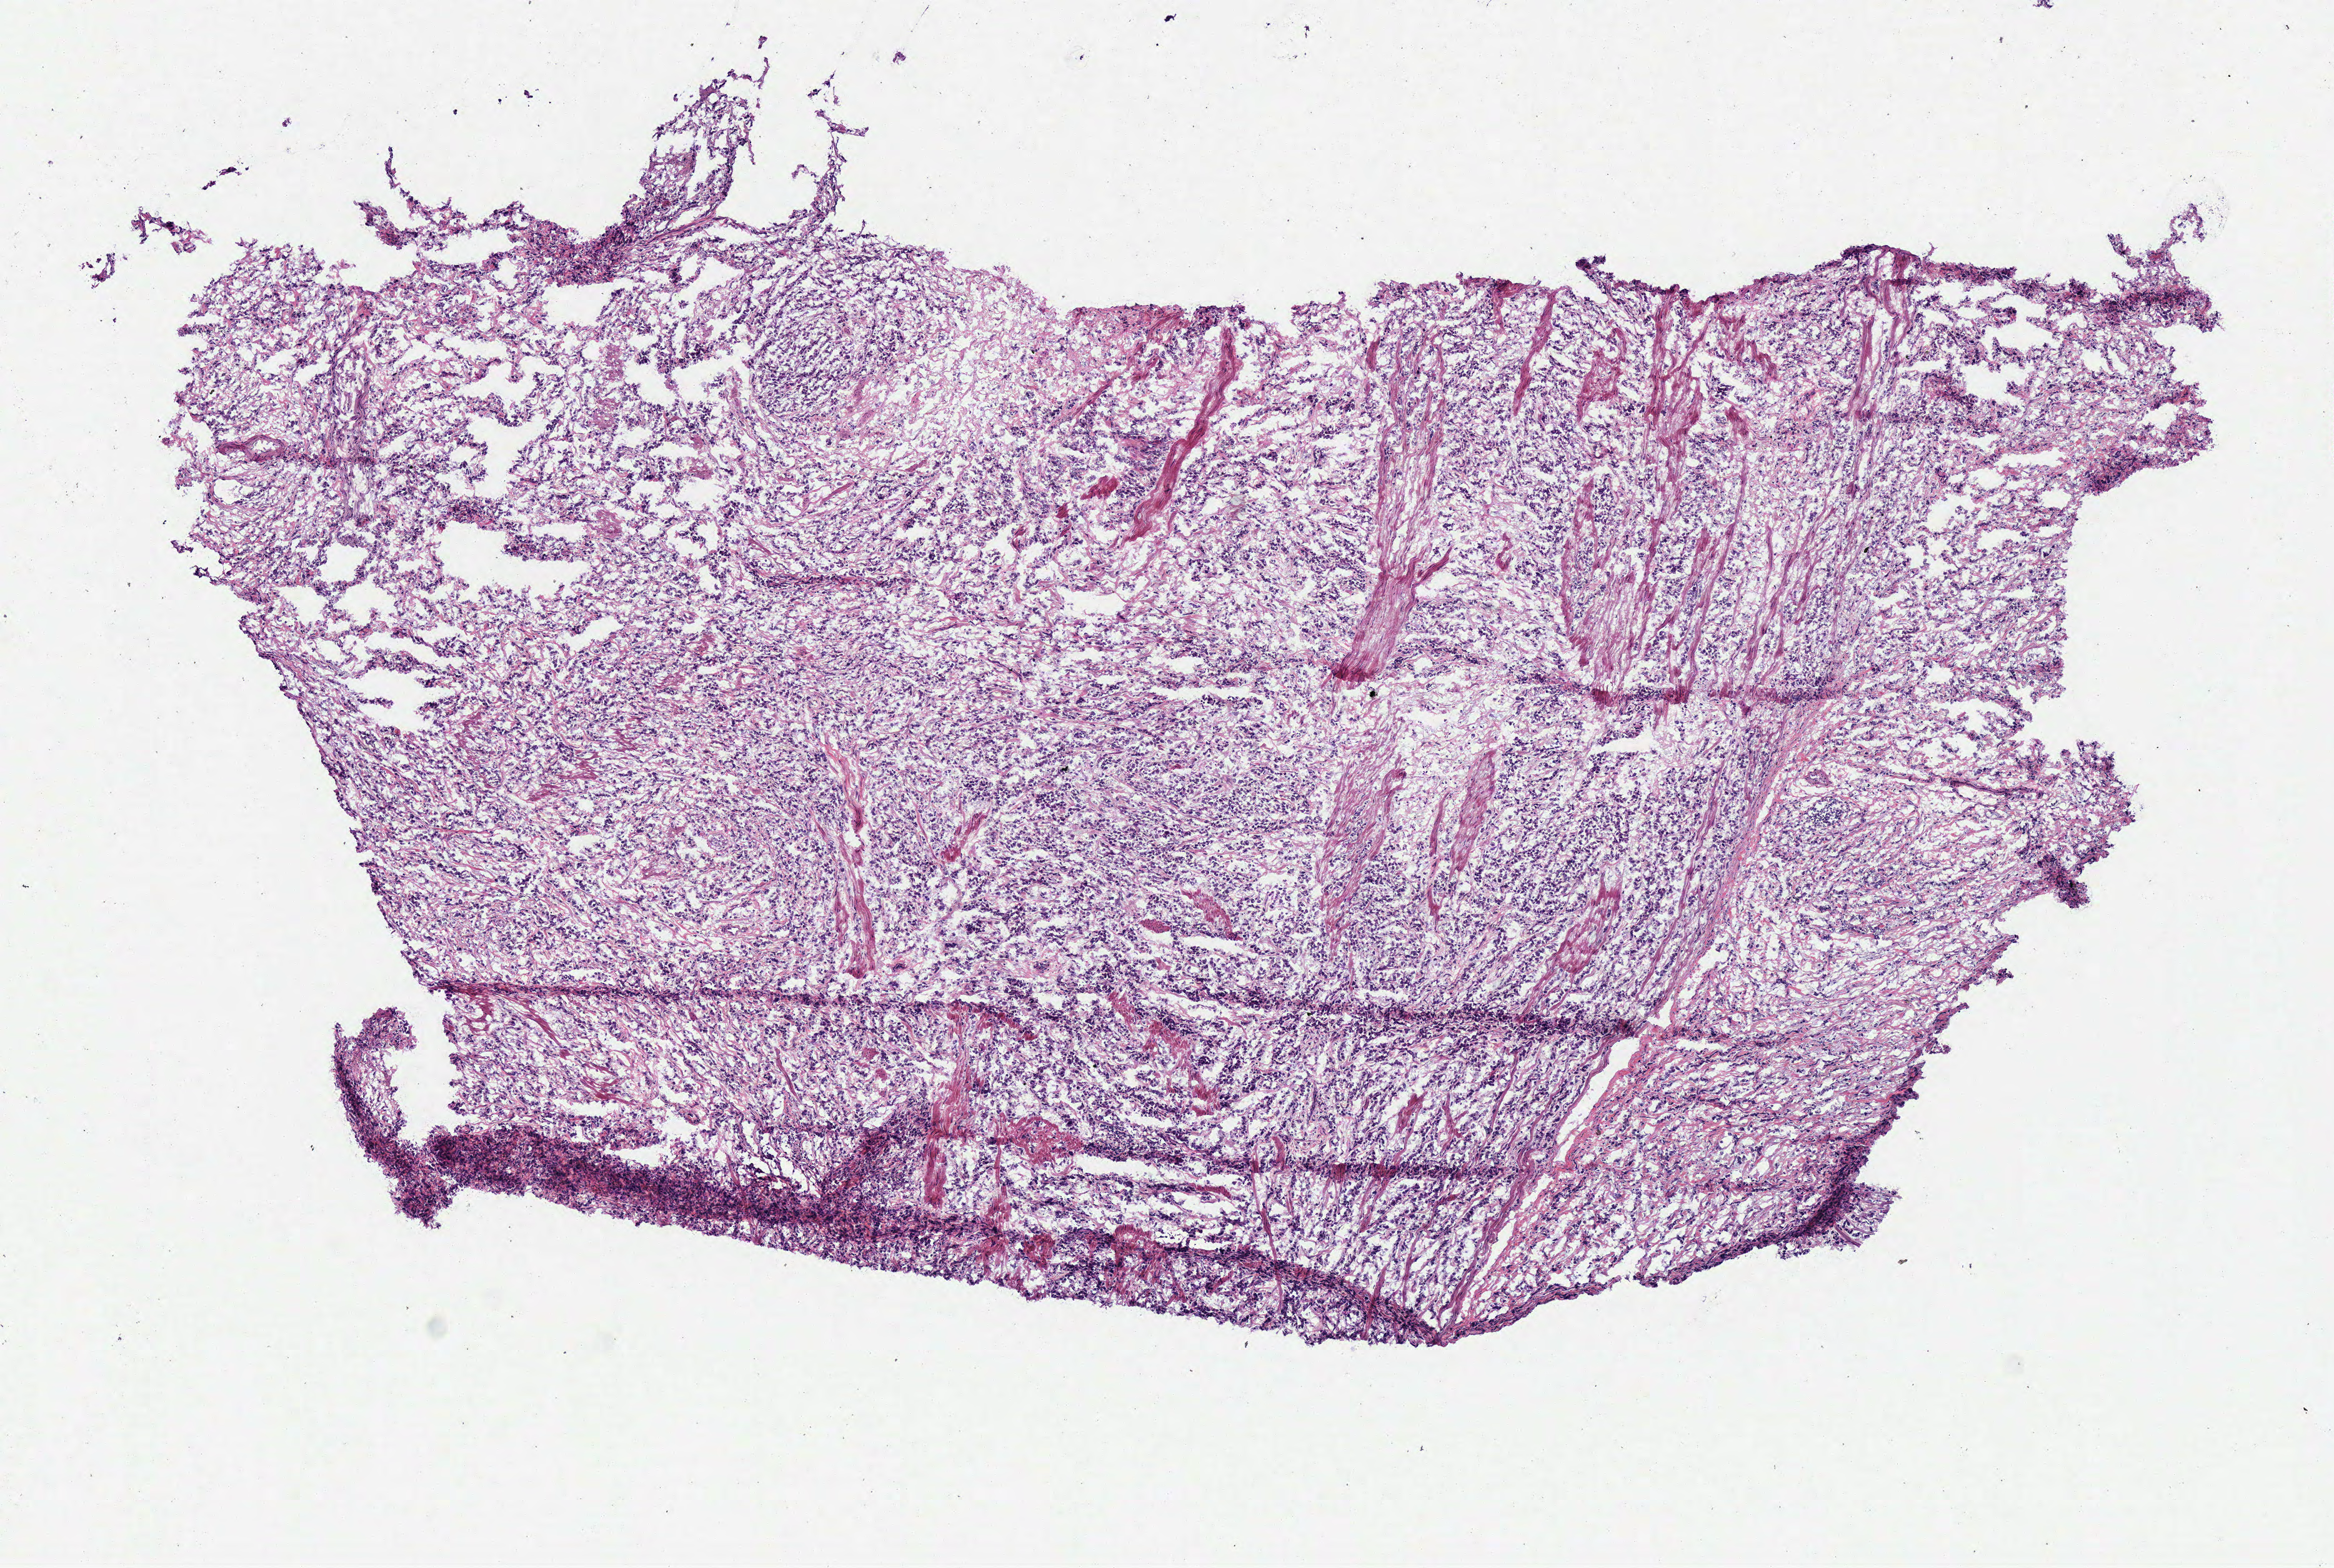
Whole-slide histology image, Hematoxylin and eosin (H&E) stained — whole scanned area (about 7.3 x 4.9 mm, acquisition: 40x scan) shown as a low-resolution overview. Frozen section from the bottom of the tissue portion. Stomach, primary tumour sample. Male, age 65 years at initial diagnosis. Histologic grade: G3 (poorly differentiated). Composition of this section per pathologist review: tumour cells 90%, tumour nuclei 80%, normal cells 0%, stromal cells 10%, necrosis 0%.
Pathologic diagnosis: Carcinoma, diffuse type (body of stomach). Lymph nodes positive (case pathology): 15 of 17 examined.